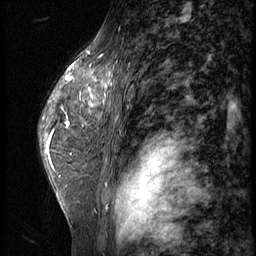
Breast MRI (dynamic contrast-enhanced), one sagittal slice. Position 41 of 62 along the scan axis. 3 images stored at this slice position (order not interpretable as contrast timing). 1.5 T. TE 4.2 ms, TR 9 ms. 2.5 mm slice thickness. 256 × 256 image matrix, field of view 180 × 180 mm. Female patient, age 44 years. Case-level facts recorded for this patient, not image findings: setting: breast cancer imaged before/during neoadjuvant chemotherapy; receptor status: triple-negative.
Annotated regions visible in this slice (semi-automatically segmented with operator editing):
- analysis volume of interest (the breast-tissue region the enhancement analysis was run in; not a lesion): box from (x=73, y=64) to (x=116, y=125) px
- tumour enhancement mask (voxels above the 140 % enhancement threshold inside the analysis volume of interest): (x=81, y=68)–(x=114, y=110)